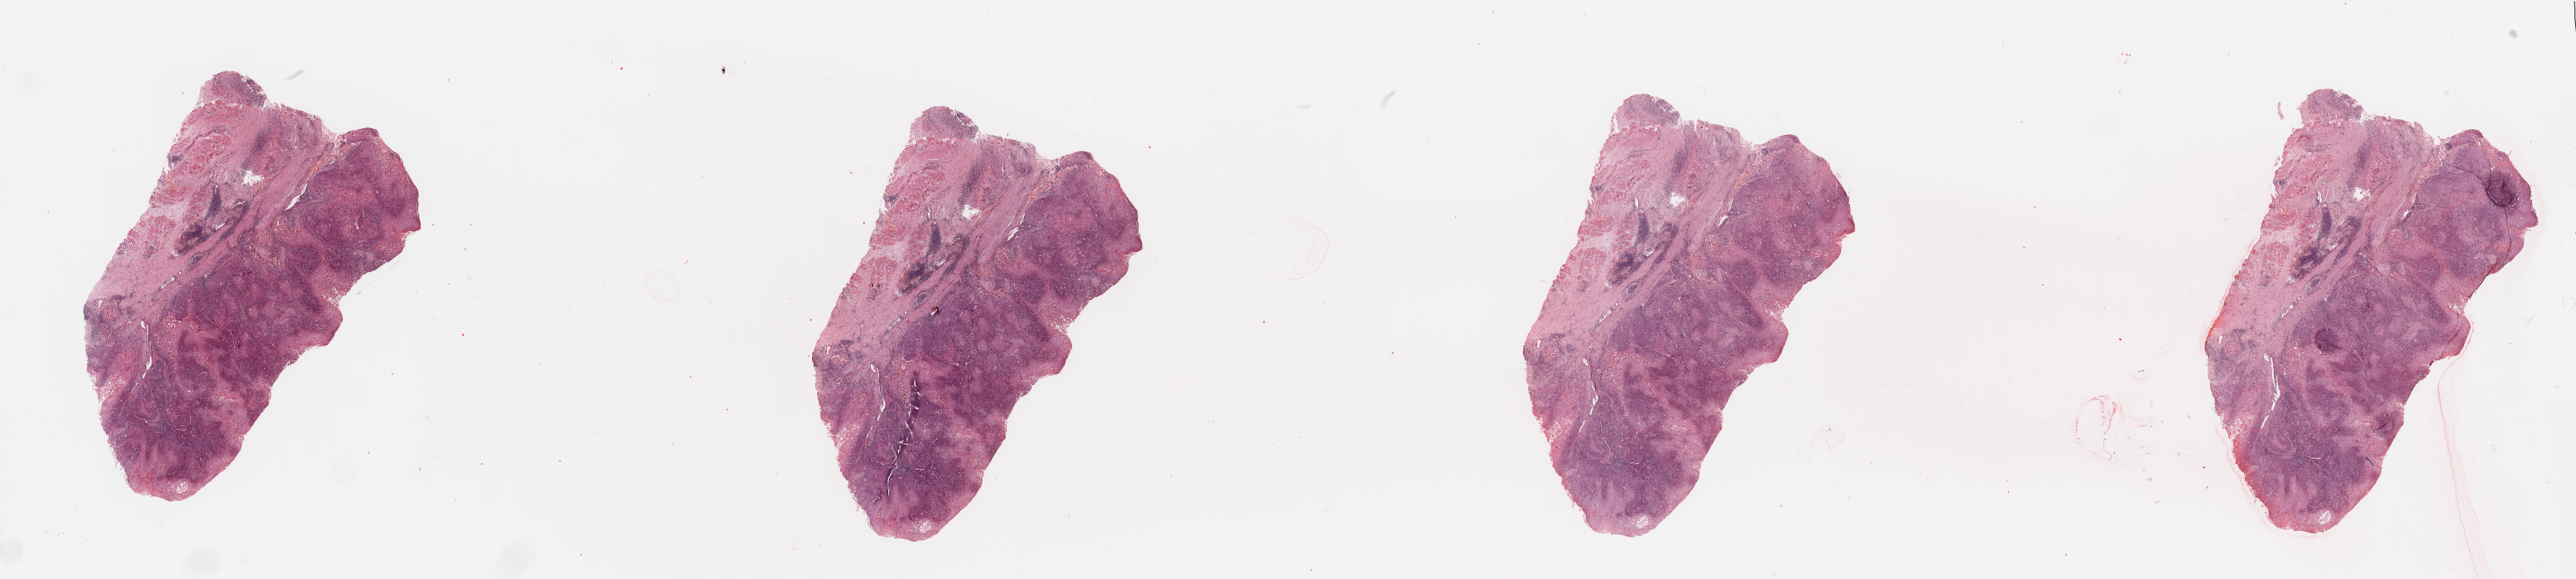
Whole-slide histology image, H&E-stained, shown as a low-resolution overview of the whole scanned area (about 49.2 x 11.1 mm). Head and neck, tissue type not recorded. Patient: male, age 81 years.
Patient diagnosis: Squamous cell carcinoma, NOS.